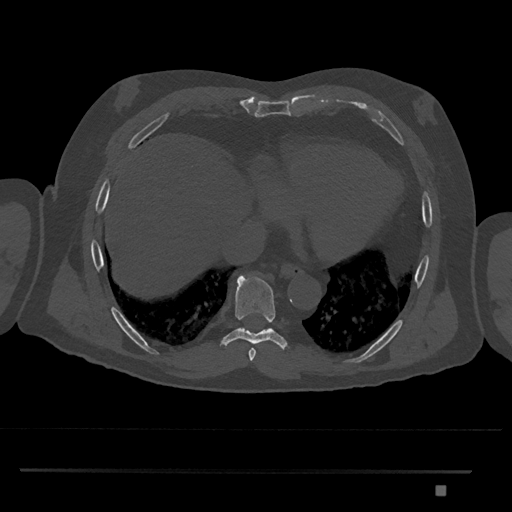
CT including the spine, one axial slice; position 1111 of 1134 along the scan axis; reconstruction kernel Br40s/3; 120 kVp; bone window (W 1800 / L 400 HU); 0.5 mm slice thickness; 512 × 512 image matrix, field of view 429 × 429 mm. Male patient, age 65 years. Case-level facts recorded for this patient, not image findings: primary cancer: prostate.
Outlined on this slice (semi-automatic segmentation, software-assisted and operator-edited):
- T8 vertebra: bounding box [x1, y1, x2, y2] px = [222, 274, 287, 349]